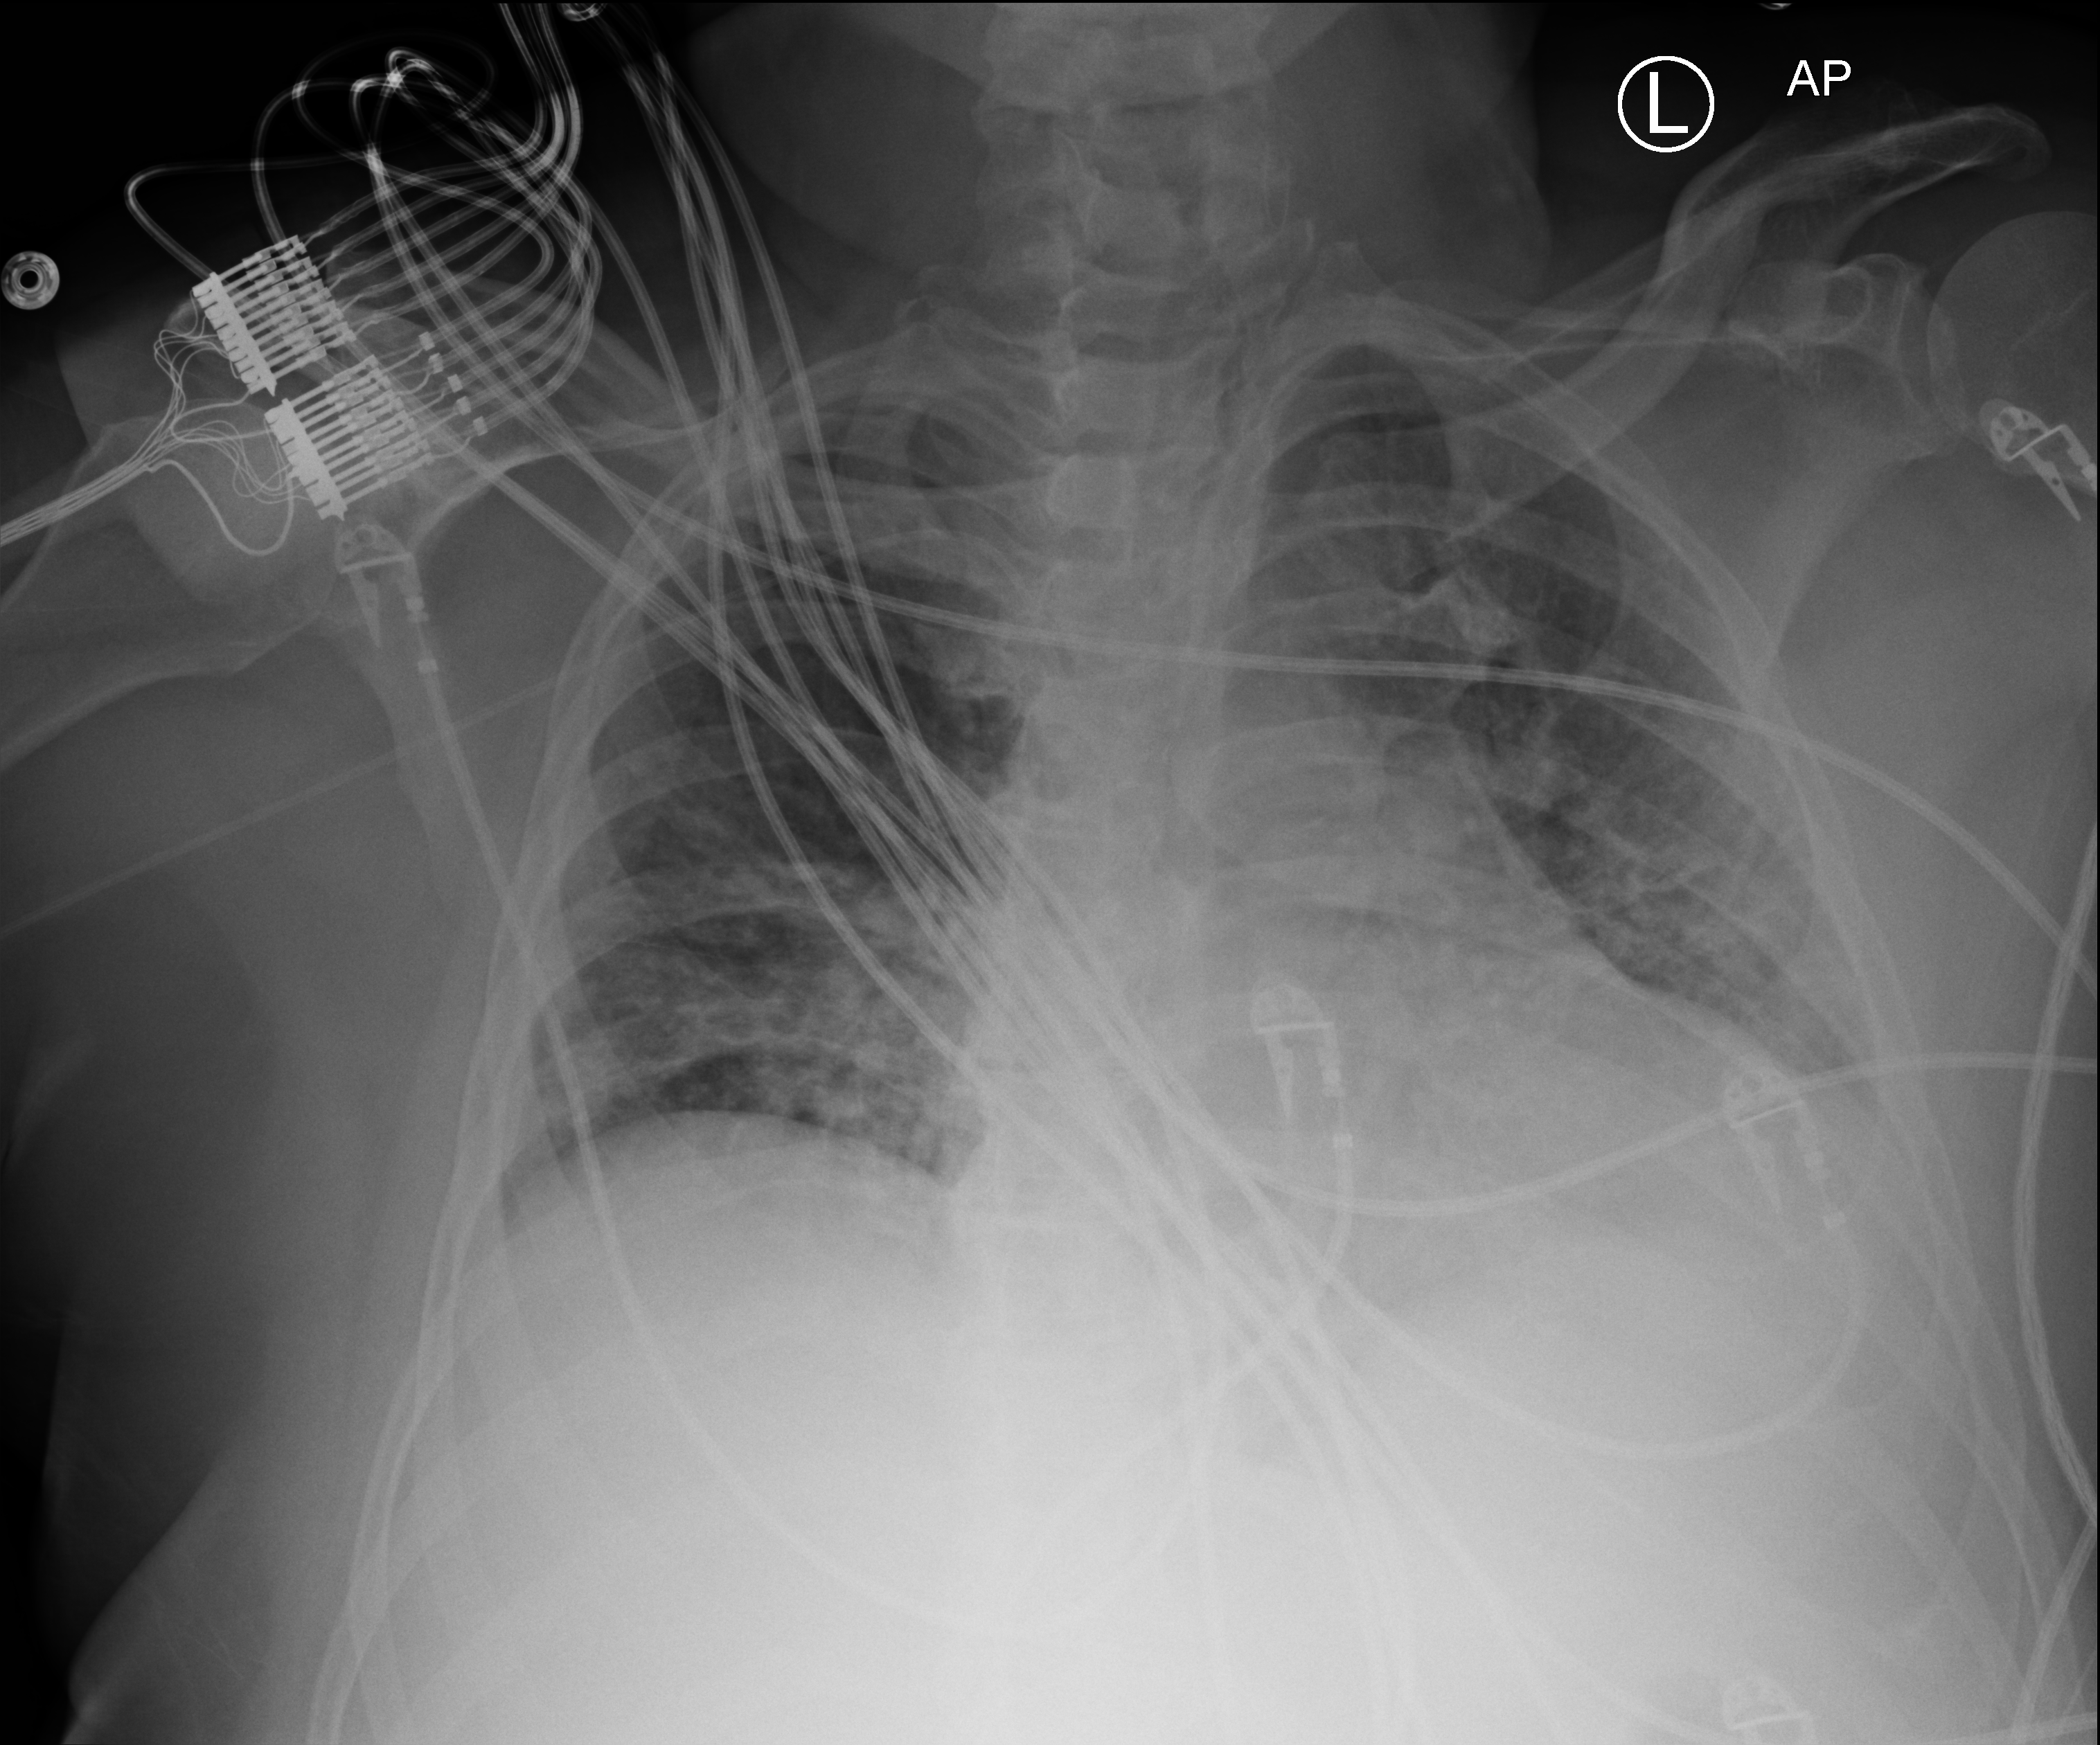
Bedside chest radiograph (computed radiography), anteroposterior (AP) projection. Male patient hospitalised with COVID-19, age 18–59 years.
Admission-level facts for this patient (not findings on this image; timing relative to this image not recorded): chronic kidney disease (admission record): no; admitted to intensive care during this hospital stay: yes; mechanically ventilated during this hospital stay: yes.